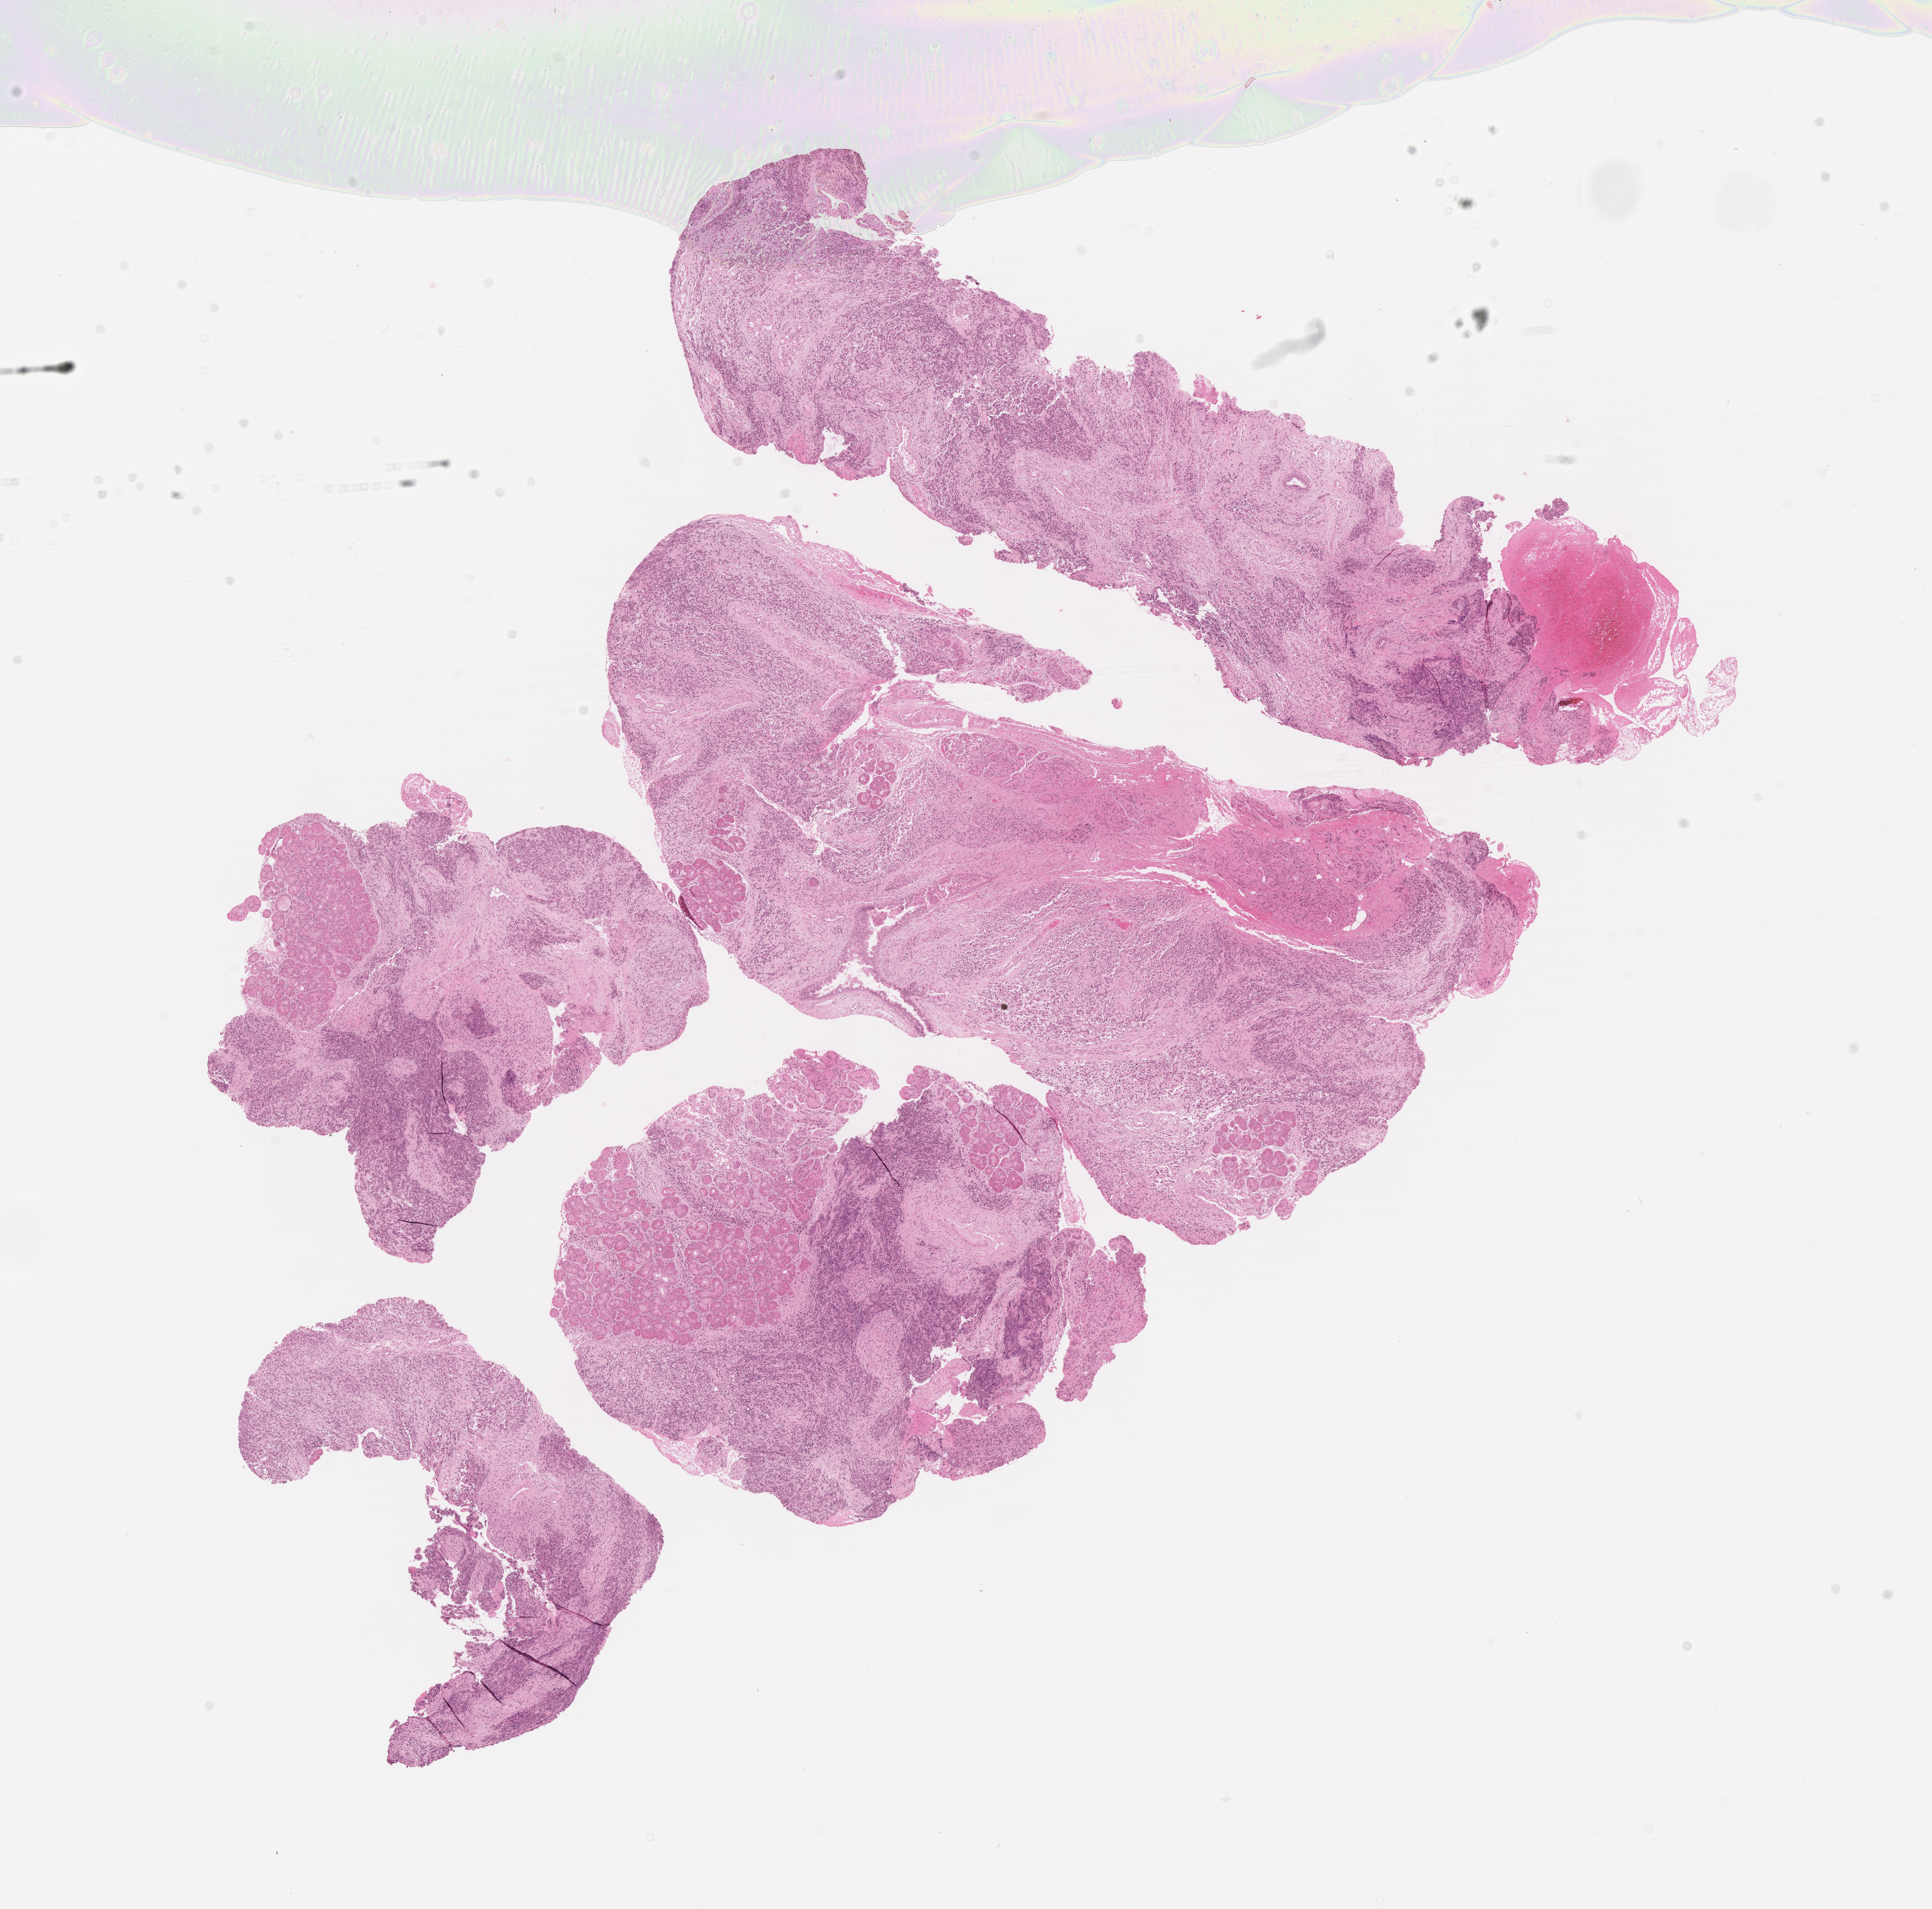
Digitized H&E-stained section of tumor tissue — shown as a low-resolution overview of the whole scanned area (about 11.1 x 10.9 mm). Formalin-fixed, paraffin-embedded (FFPE) tissue. Site: eye, orbit-left. Female patient, age at diagnosis 6.2 years.
- metastatic status at presentation (as recorded): non-metastatic
- diagnosis: rhabdomyosarcoma; histological classification: embryonal rhabdomyosarcoma
- stage (as recorded): 1